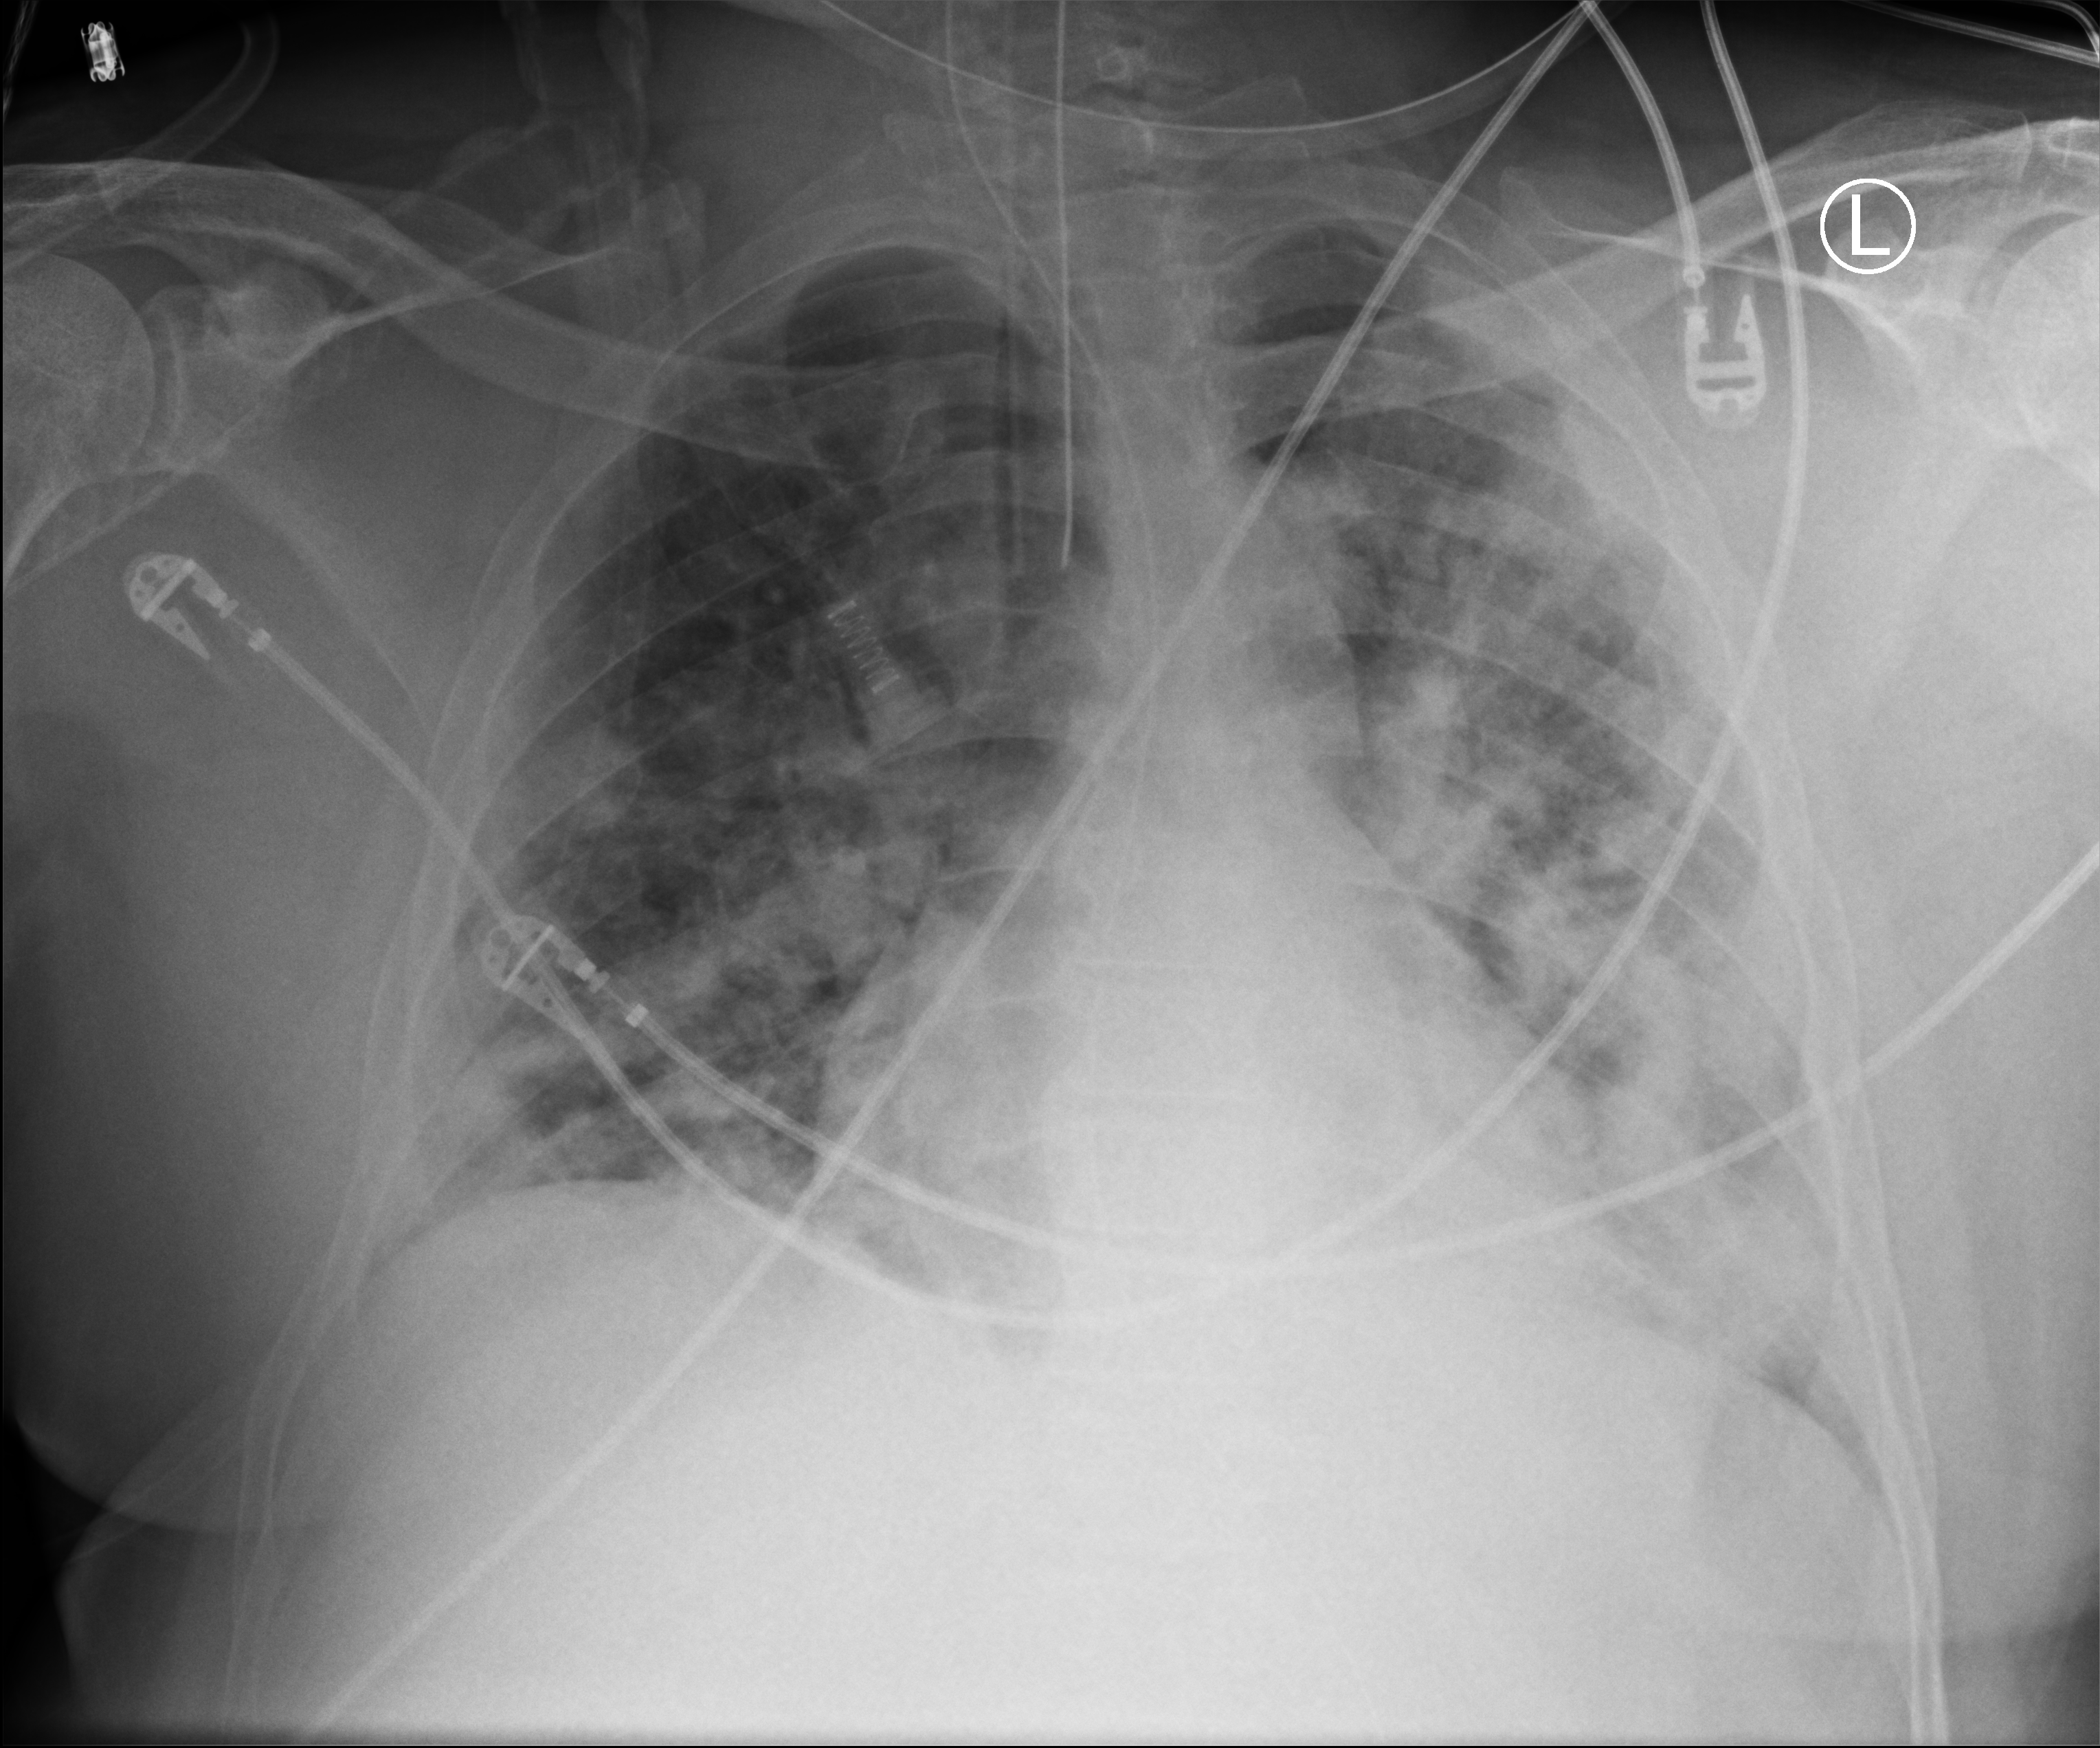
Portable chest radiograph, anteroposterior (AP) projection. Patient hospitalised with COVID-19; male, aged 18–59 years.
Admission-level facts for this patient (not findings on this image; timing relative to this image not recorded):
- COPD (admission record): yes